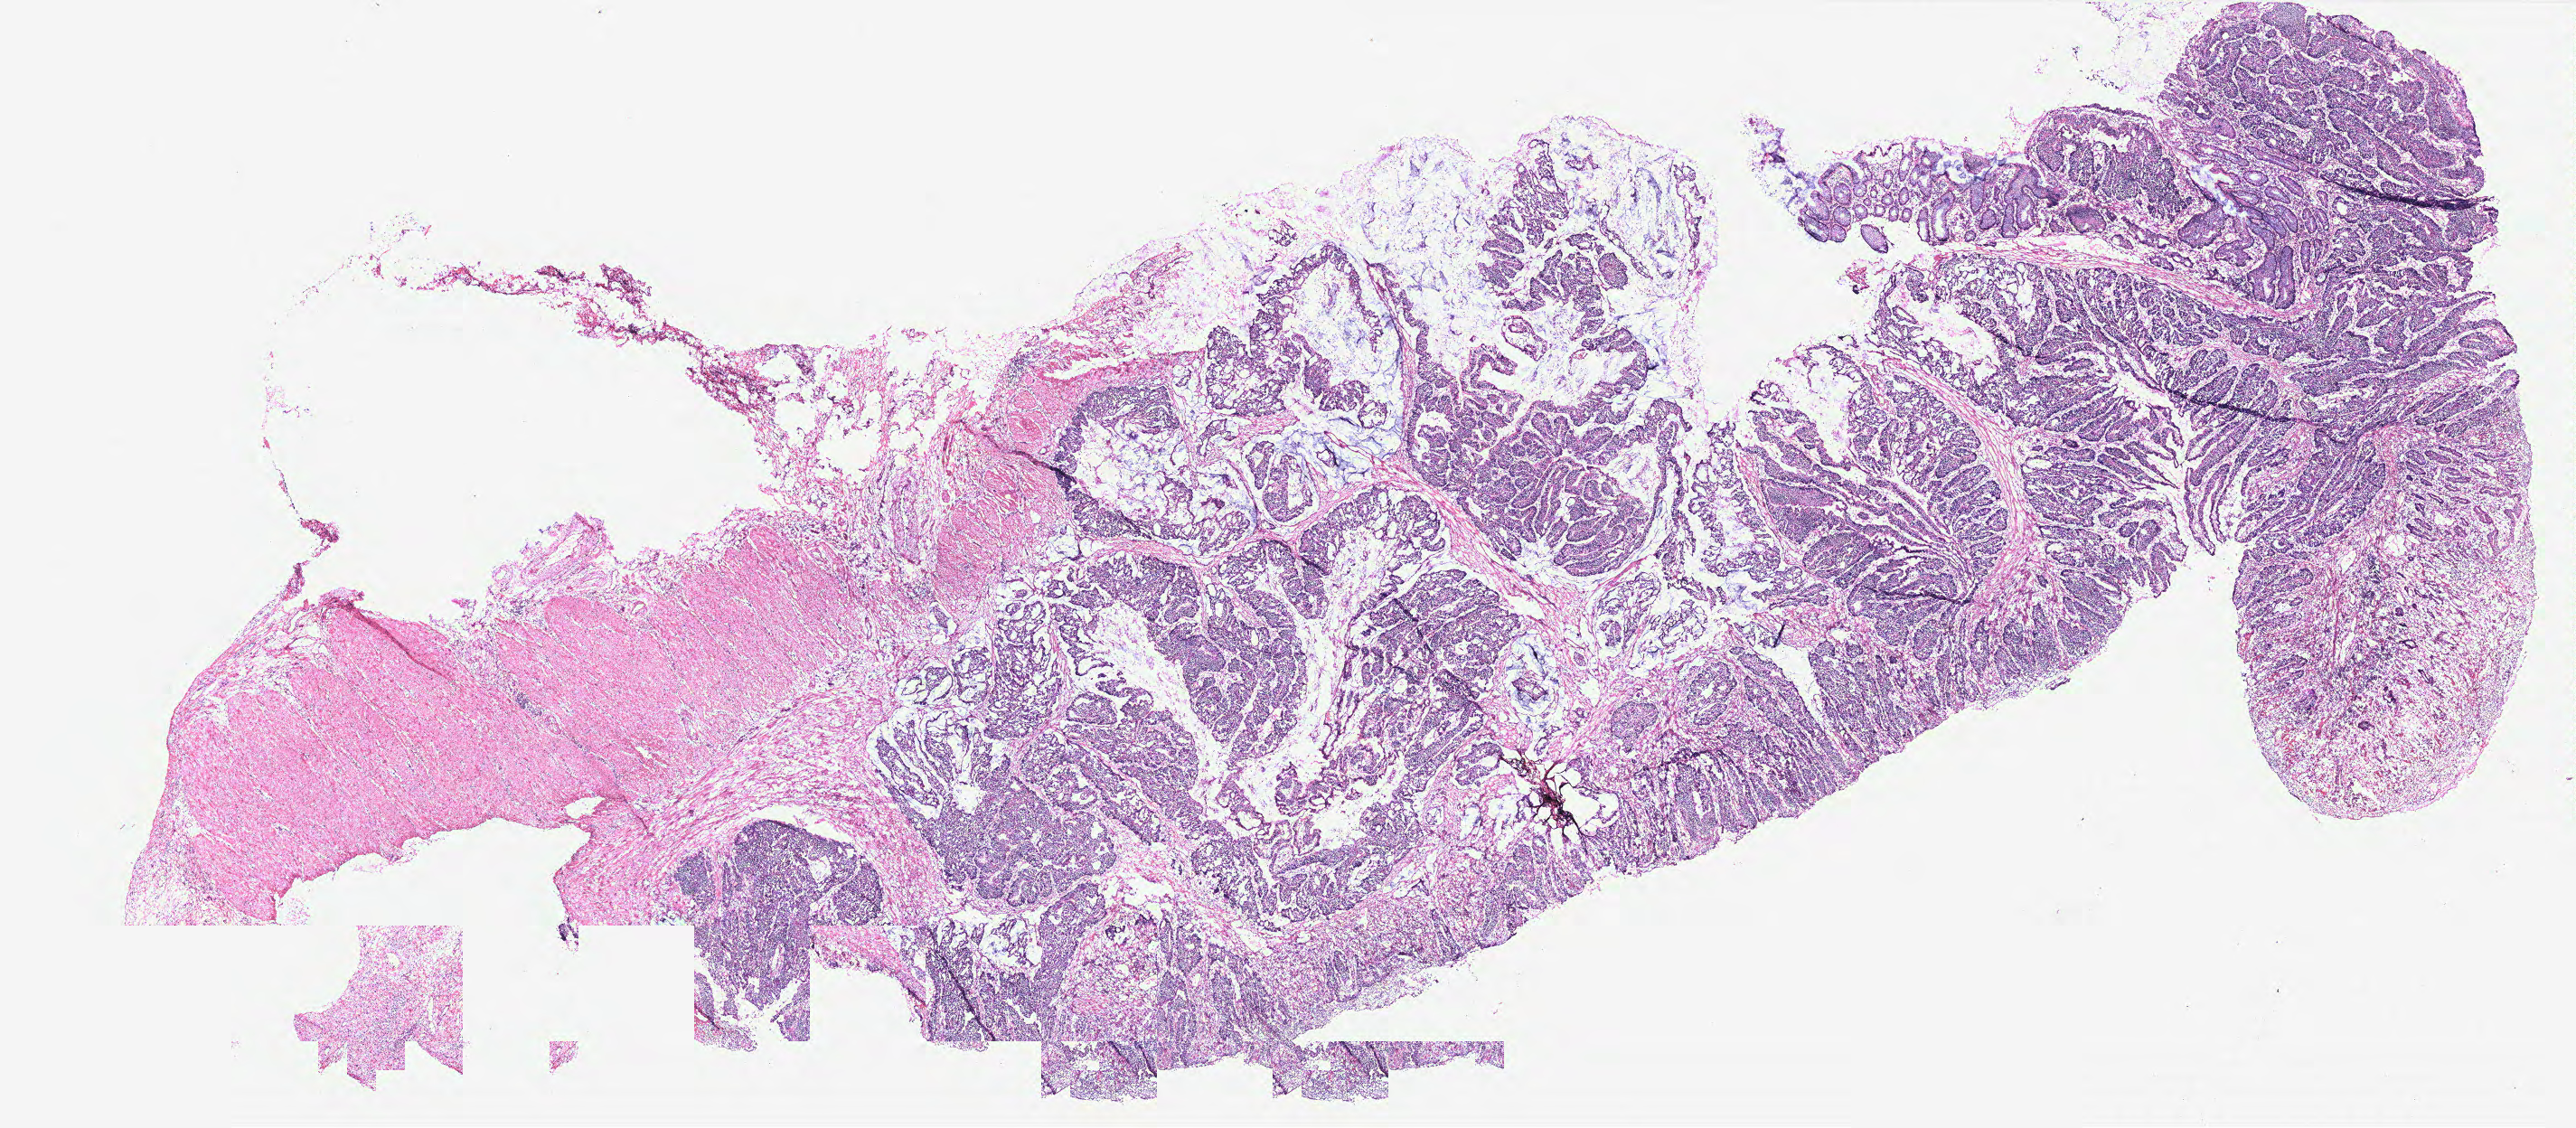
Whole-slide histology image, H&E, a low-resolution overview of the entire scanned area, about 22.8 x 10.0 mm (from a 40x scan). Colon, tissue type not recorded.
- patient diagnosis (cohort enrolment): colon cancer (colon)